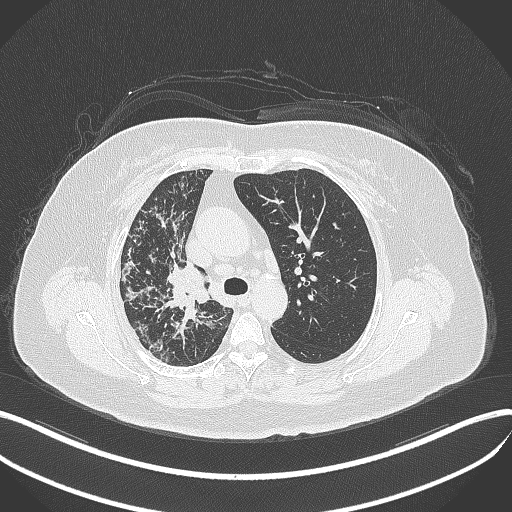
Chest CT, one axial slice. Position 246 of 376 along the scan axis. Reconstruction kernel B70f. 120 kVp. Lung window (W 1500 / L -600 HU). 1 mm slice thickness. 512 × 512 image matrix, field of view 400 × 400 mm. Female patient, age 60 years. Case-level facts recorded for this patient, not image findings: clinical TNM (as recorded): T1c N0 M0; histopathological grade: G1-G2.
Annotated regions visible in this slice (rectangle marked by the reading radiologist):
- lung tumour (recorded histology: squamous cell carcinoma): bounding box <162,261,215,311> (left, top, right, bottom; pixels)